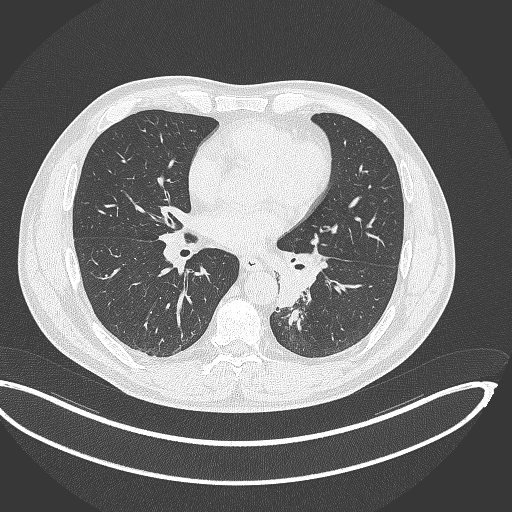
Chest CT, one axial slice. Slice 167 of 362 in the series (ordered by position). Reconstruction kernel B70f. Lung window (W 1500 / L -600 HU). 1 mm slice thickness. 512 × 512 image matrix. Male patient, age 50 years. From the clinical record (not read from this slice): clinical TNM (as recorded): T2a N3 M0.
Annotated regions visible in this slice (bounding box drawn by a radiologist):
- lung tumour (recorded histology: squamous cell carcinoma): bounding box [x1, y1, x2, y2] px = [271, 248, 333, 315]